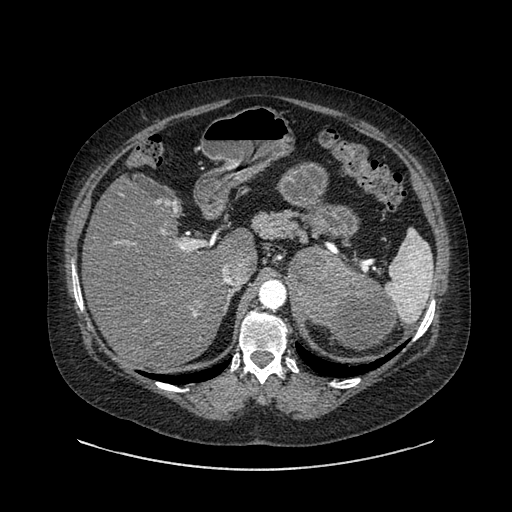
Contrast-enhanced abdominal CT, one axial slice. 120 kVp. Soft-tissue window (W 400 / L 40 HU). 0.62 mm slice thickness. 512 × 512 image matrix. Patient: female, 61 years. Case-level facts recorded for this patient, not image findings: diagnosis: adrenocortical carcinoma; tumour side: left adrenal; tumour size at pathology: 13 cm; Ki-67 index: 79 %; stage (as recorded): 2.
Outlined on this slice (semi-automatic segmentation, software-assisted and operator-edited):
- mass: bounding box <289,250,394,349> (left, top, right, bottom; pixels)